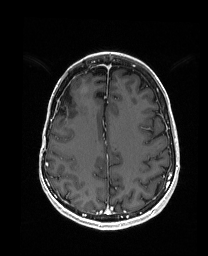
Brain MRI from a brain-tumour surgery series, one axial slice. T1-weighted post-contrast. 208 × 256 image matrix. From the clinical record (not read from this slice): histopathology: Metastatic Carcinoma from Breast primary; tumour location: Right Frontal.
Outlined on this slice (outlined manually by an expert reader):
- previous resection cavity: box from (x=60, y=84) to (x=72, y=105) px
- tumour: (x=81, y=88)–(x=86, y=91)